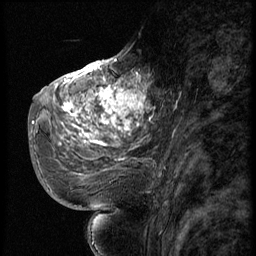
Breast MRI (dynamic contrast-enhanced), one sagittal slice. Position 29 of 56 along the scan axis. 3 images stored at this slice position (order not interpretable as contrast timing). 1.5 T. TE 4.2 ms, TR 9 ms. 2.5 mm slice thickness. 256 × 256 image matrix, field of view 180 × 180 mm. Patient: female, 51 years. Case-level facts recorded for this patient, not image findings: setting: breast cancer imaged before/during neoadjuvant chemotherapy; receptor status: triple-negative.
Outlined on this slice (semi-automatically segmented with operator editing):
- analysis volume of interest (the breast-tissue region the enhancement analysis was run in; not a lesion): bounding box <52,66,147,179> (left, top, right, bottom; pixels)
- tumour enhancement mask (voxels above the 140 % enhancement threshold inside the analysis volume of interest): <63,68,146,143>